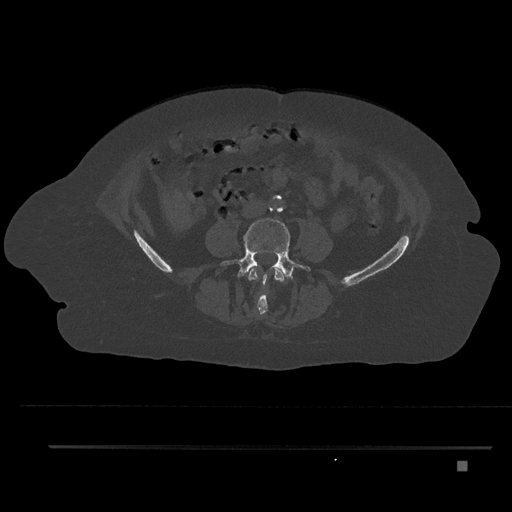
CT including the spine, one axial slice; position 92 of 797 along the scan axis; reconstruction kernel Br40s/3; 120 kVp; bone window (W 1800 / L 400 HU); 512 × 512 image matrix, field of view 437 × 437 mm. Female patient, age 76 years. From the clinical record (not read from this slice): primary cancer: lung.
Annotated regions visible in this slice (semi-automatically segmented with operator editing):
- L3 vertebra: bounding box [x1, y1, x2, y2] px = [248, 267, 285, 315]
- L4 vertebra: [220, 218, 311, 301]